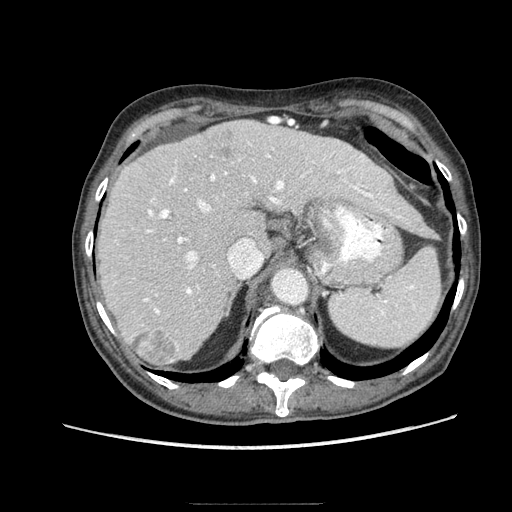
Contrast-enhanced abdominal CT (liver protocol), one axial slice; slice 60 of 83 in the series (ordered by position); soft-tissue window (W 400 / L 40 HU); 2.5 mm slice thickness; 512 × 512 image matrix, field of view 360 × 360 mm. Case-level facts recorded for this patient, not image findings: diagnosis: hepatocellular carcinoma (patient treated with transarterial chemoembolisation; whether this scan precedes or follows treatment is not stated here); TNM stage (as recorded): Stage-I; Child-Pugh class: A.
Annotated regions visible in this slice (semi-automatically segmented with operator editing):
- abdominal aorta: box from (x=272, y=269) to (x=307, y=303) px
- liver parenchyma outside the tumour (the mass and vessels are separate outlines, so this box may not span the whole liver): (x=98, y=120)–(x=424, y=366)
- mass: (x=131, y=330)–(x=180, y=366)
- liver vessels: (x=143, y=142)–(x=402, y=362)